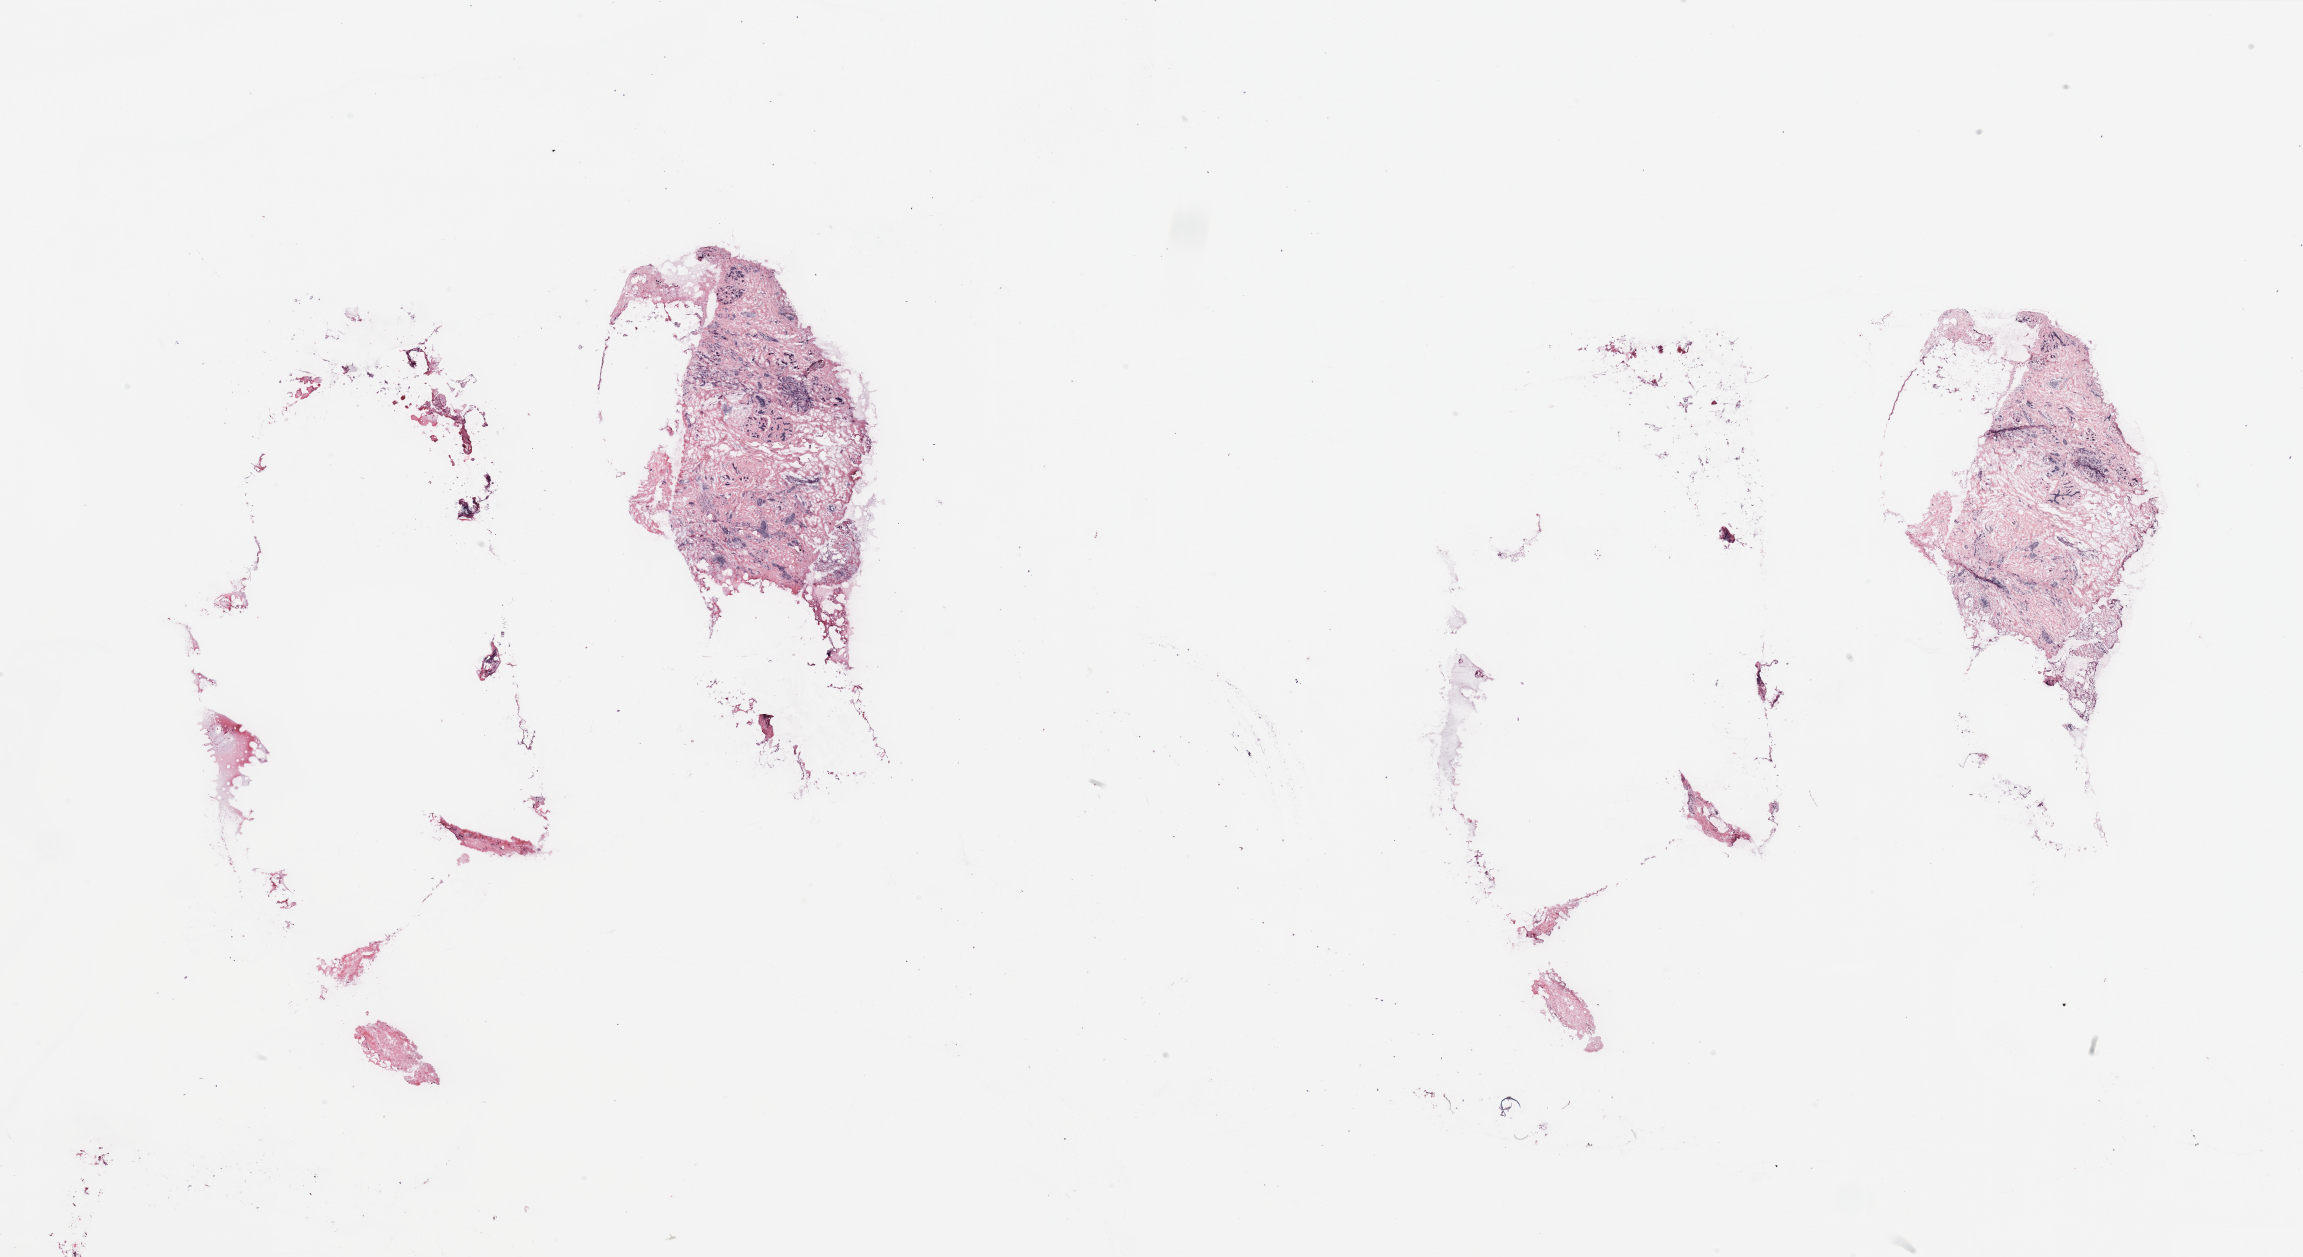
Digitized Hematoxylin and eosin (H&E) stained tissue section (whole slide), shown as a low-resolution overview of the whole scanned area (about 36.4 x 19.9 mm, from a 20x scan), breast, tissue type not recorded.
Patient diagnosis (cohort enrolment): breast cancer (breast).